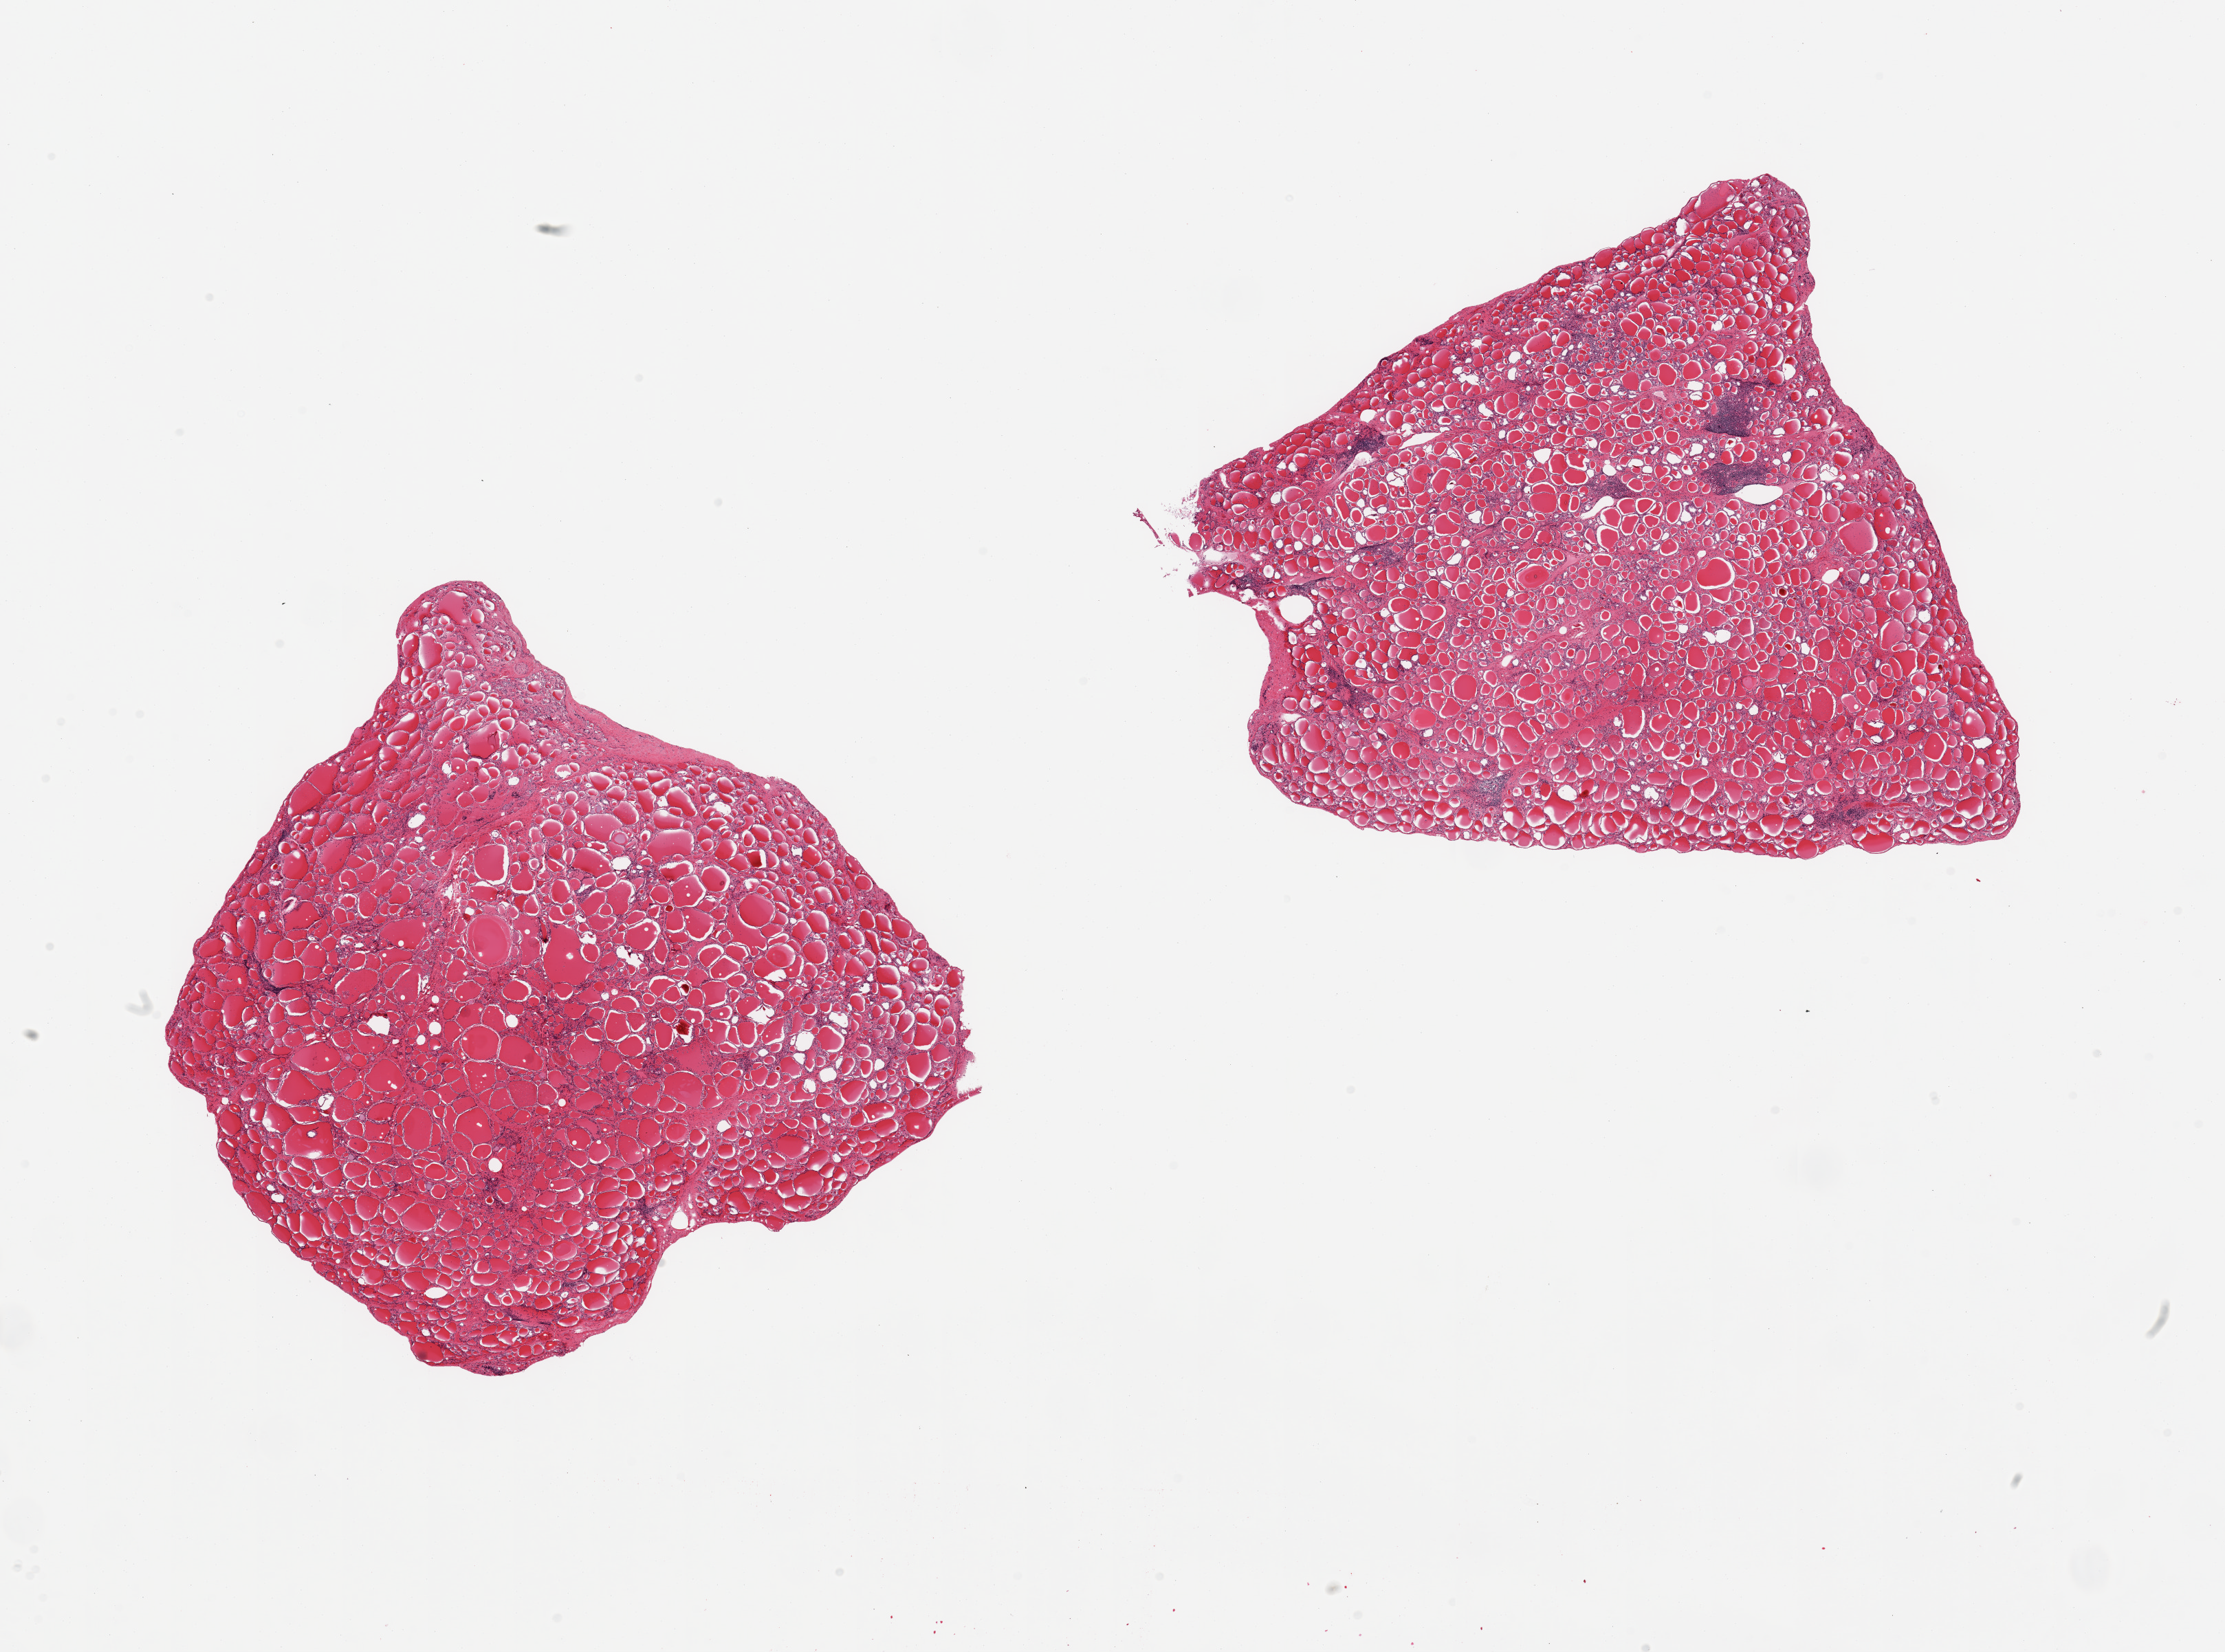
Digitized hematoxylin and eosin (H&E)-stained section, low-resolution overview of the scanned area, about 25.6 x 19.0 mm (slide scanned at 20x). PAXgene-fixed paraffin-embedded (PFPE) section. Target tissue: thyroid. Tissue donor sample. Donor sex: female.
- review note (as recorded): 2 pieces, no abnormalities